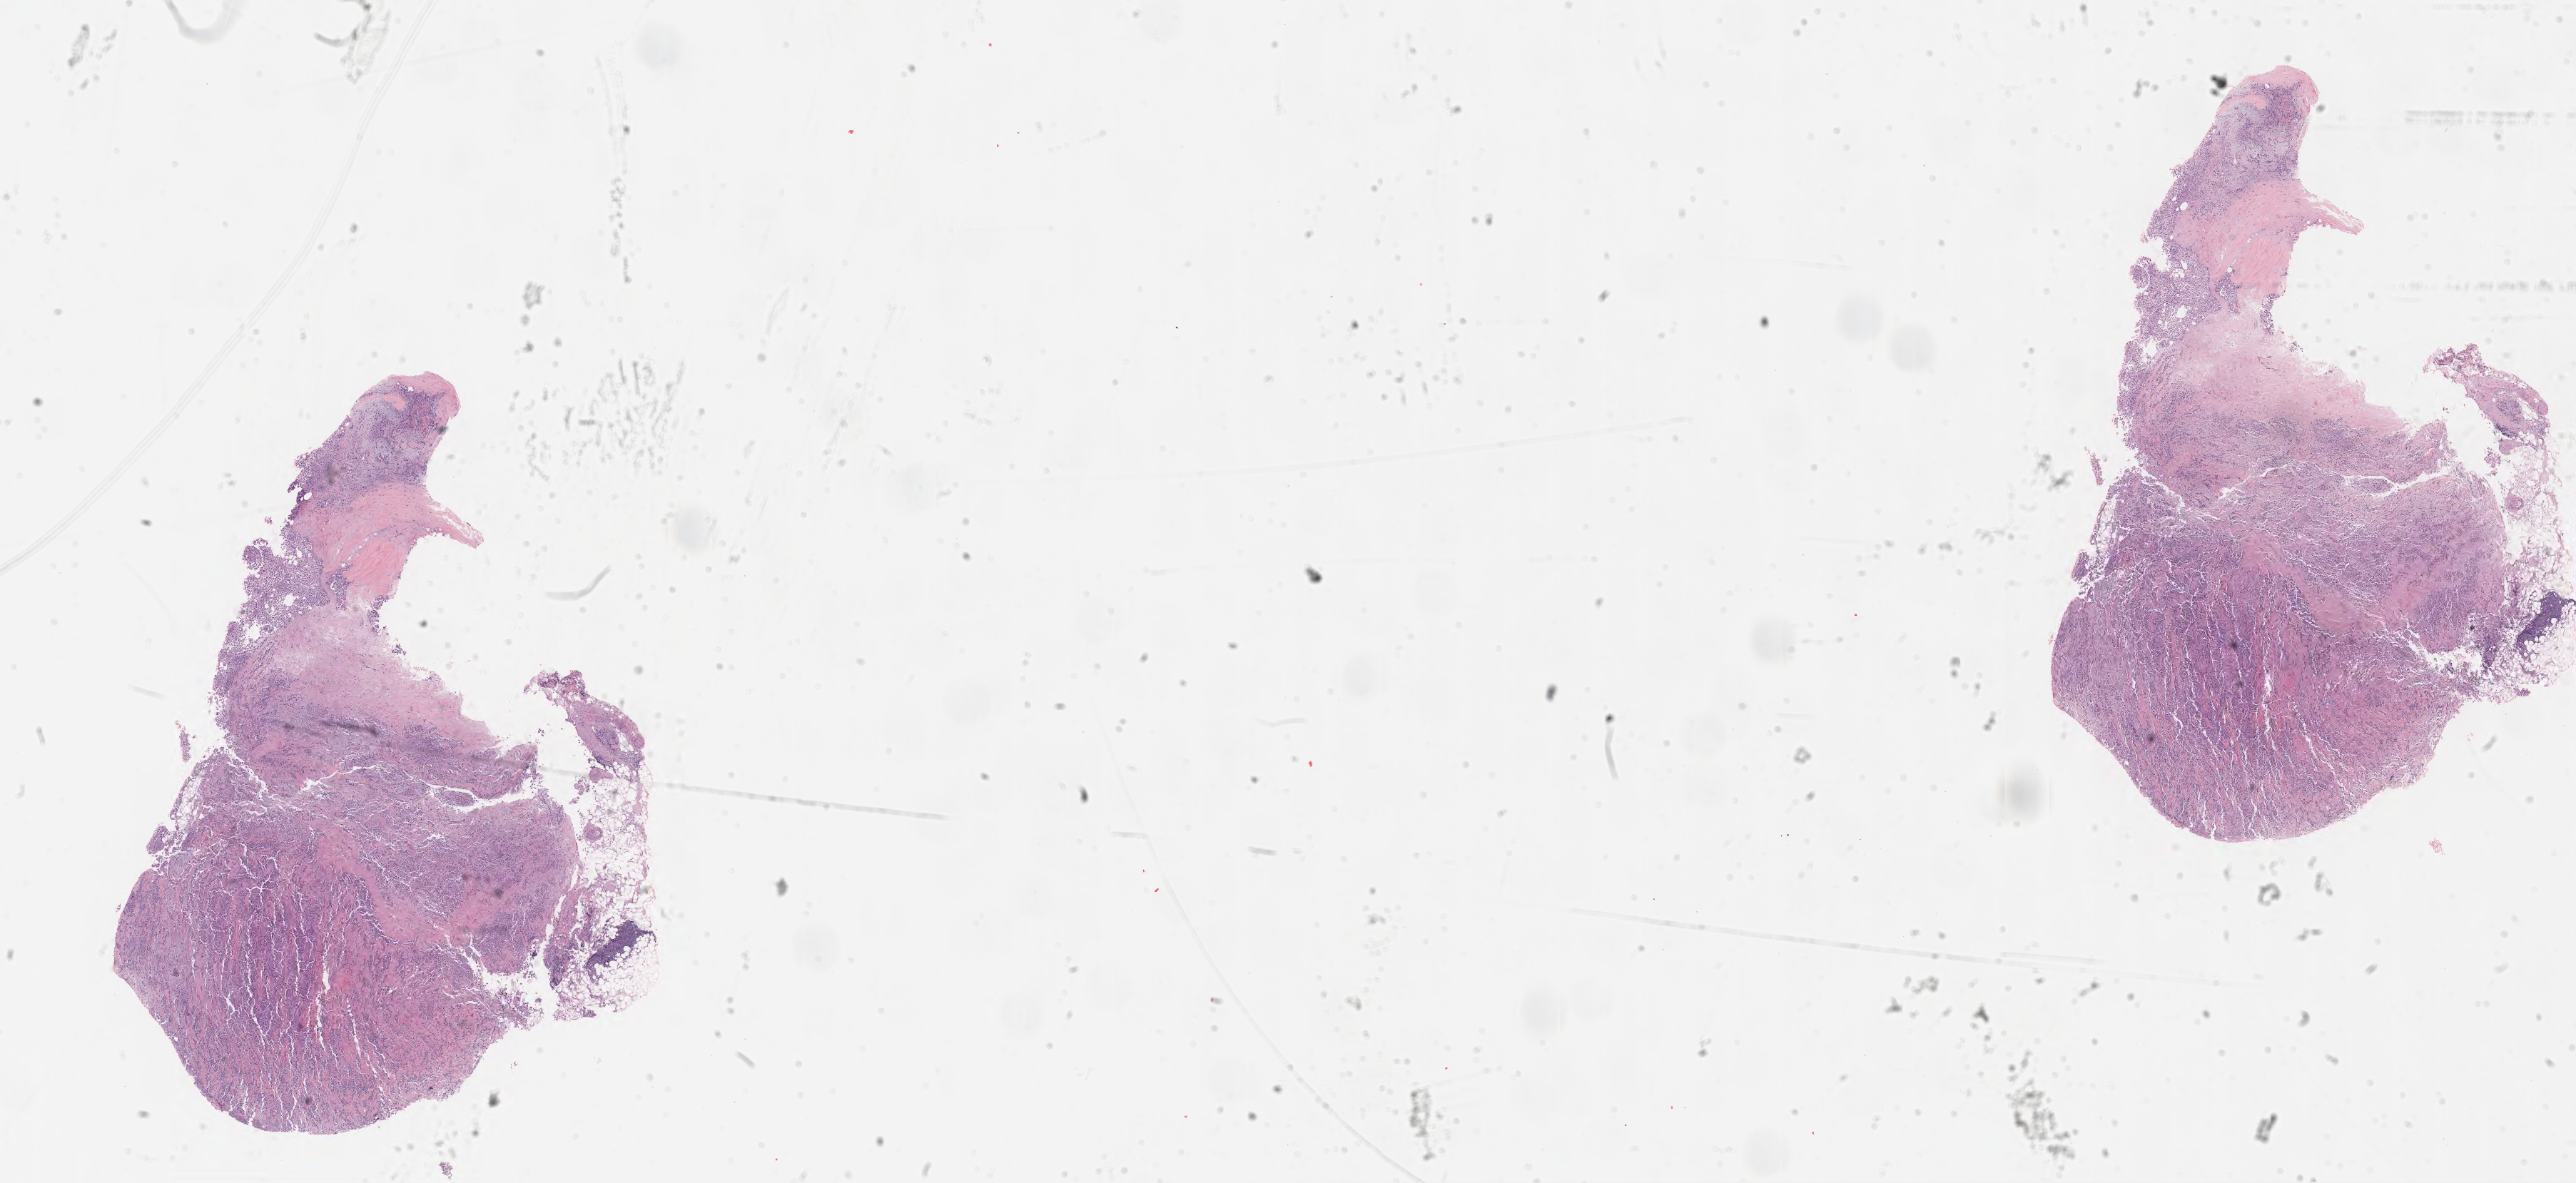
Digitized H&E tissue section (whole slide) — shown as a low-resolution overview of the whole scanned area (about 29.2 x 13.4 mm). Formalin-fixed paraffin-embedded (FFPE) diagnostic section. Primary tumour sample from the mesothelium. Male, age 71 years at initial diagnosis.
AJCC pathologic stage: III. Diagnosis: Epithelioid mesothelioma, malignant (pleura, NOS). Laterality: right.